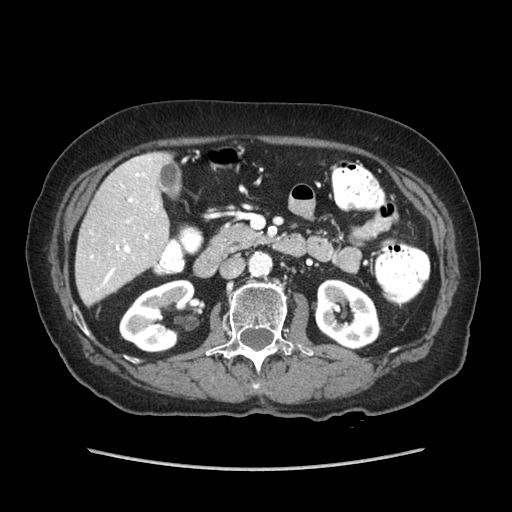
Contrast-enhanced abdominal CT (liver protocol), one axial slice. Position 25 of 89 along the scan axis. Soft-tissue window (W 400 / L 40 HU). 512 × 512 image matrix, field of view 360 × 360 mm. From the clinical record (not read from this slice): diagnosis: hepatocellular carcinoma (patient treated with transarterial chemoembolisation; whether this scan precedes or follows treatment is not stated here); TNM stage (as recorded): Stage-IIIA; Child-Pugh class: A; tumour differentiation: well differentiated.
Structures marked on this image (semi-automatically segmented with operator editing):
- liver parenchyma outside the tumour (the mass and vessels are separate outlines, so this box may not span the whole liver): box from (x=76, y=152) to (x=172, y=306) px
- liver vessels: (x=91, y=158)–(x=158, y=286)